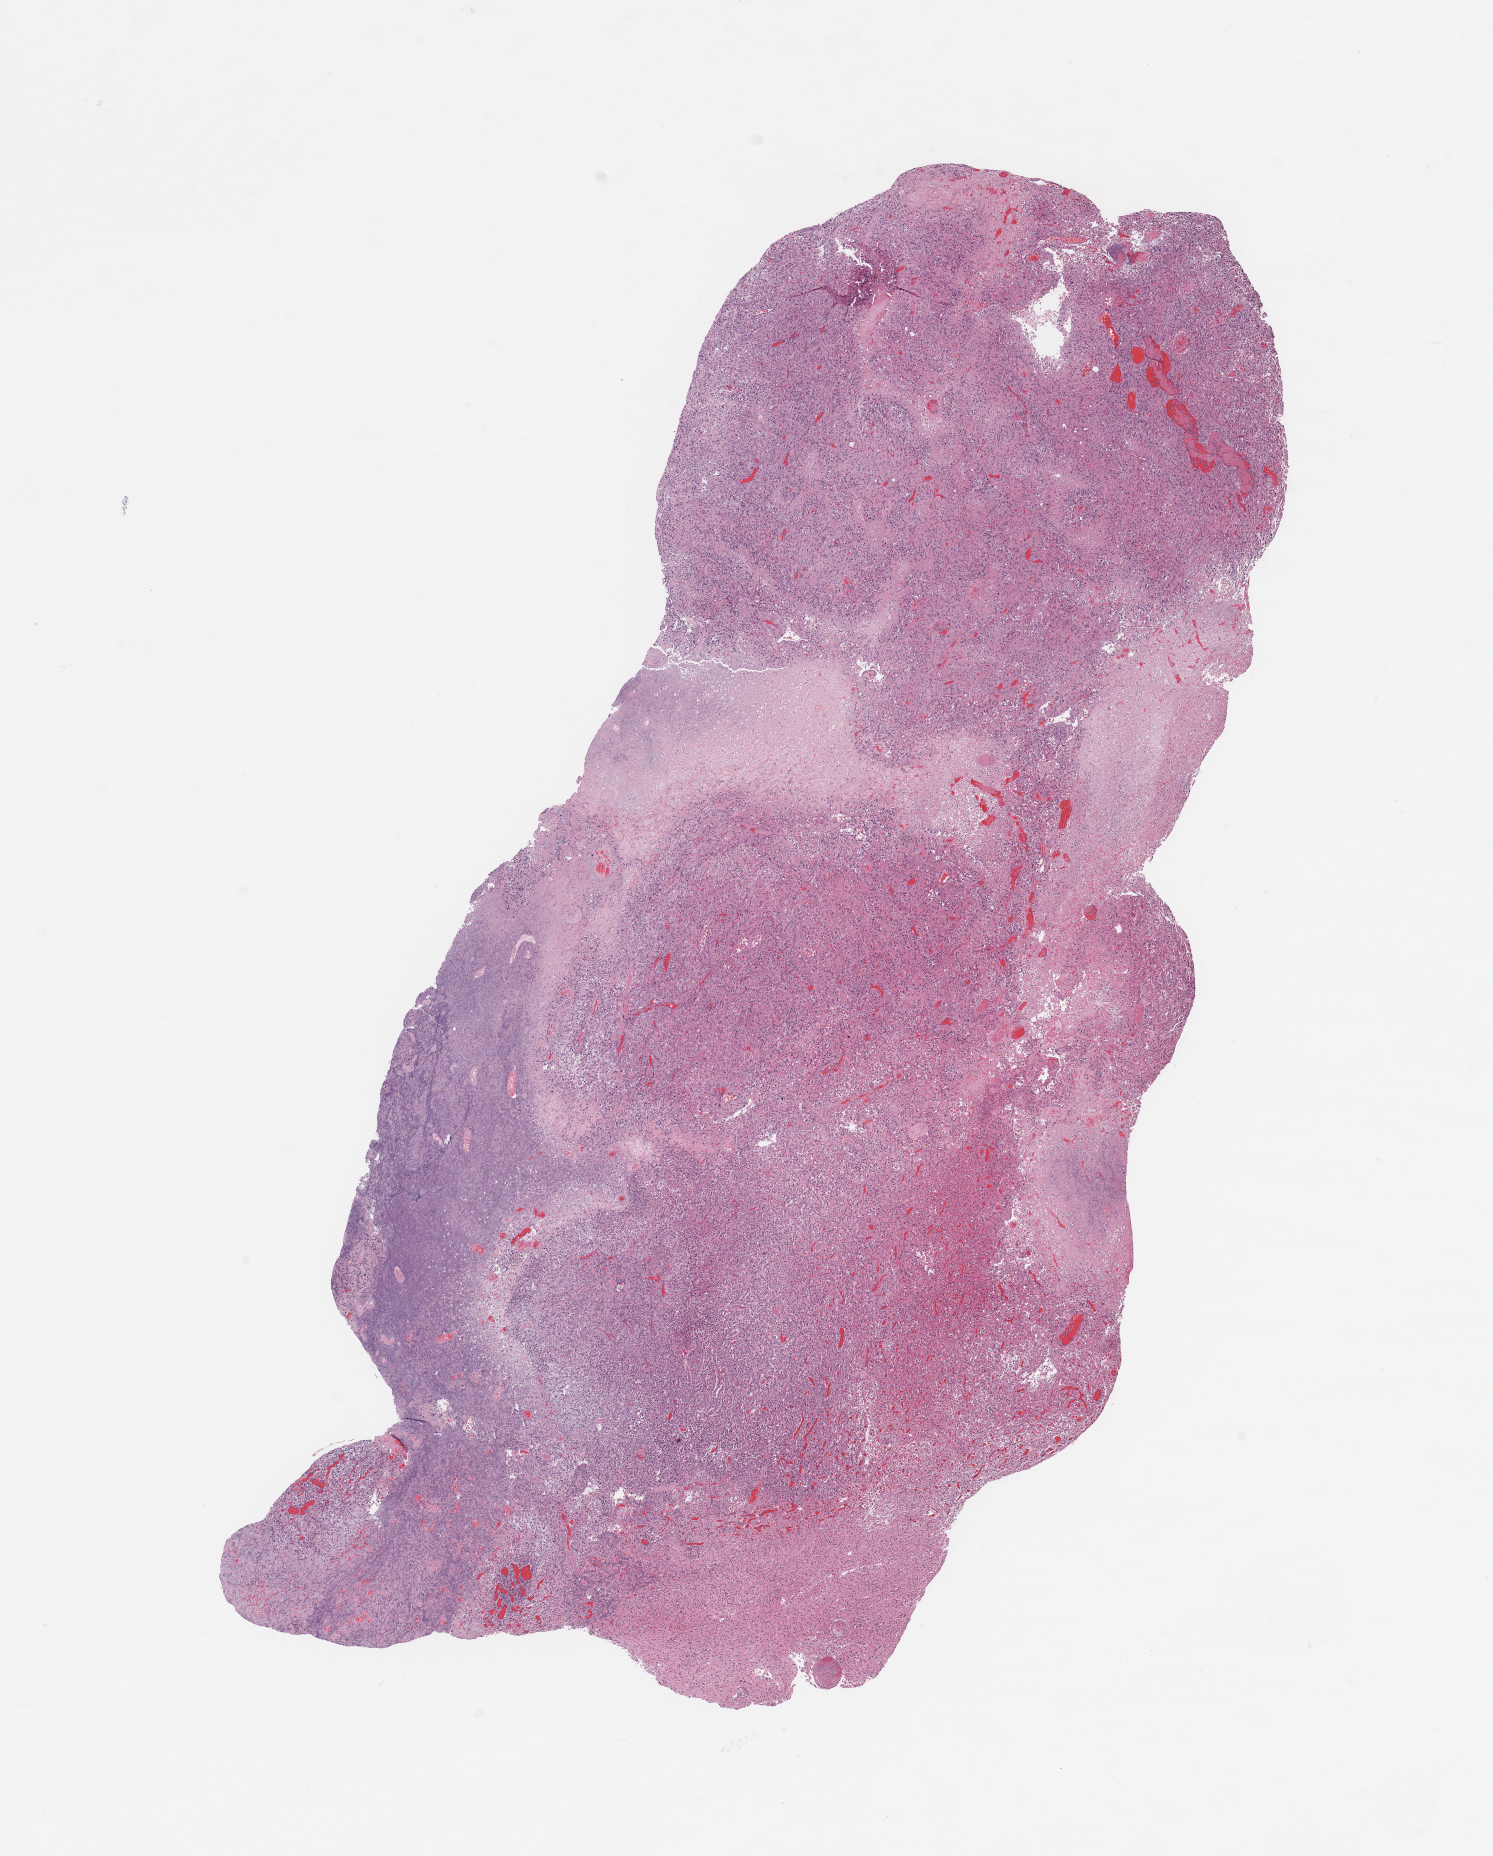
Hematoxylin and eosin (H&E) stained whole-slide image, low-resolution overview of the scanned area, about 11.8 x 14.7 mm, tumour tissue sample, brain. 62-year-old female patient.
Primary tumour site (as recorded): temporal lobe. Histologic diagnosis: Glioblastoma.